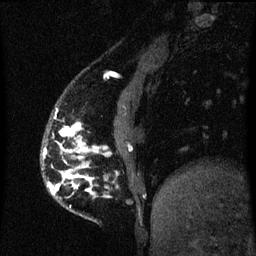
Breast MRI (dynamic contrast-enhanced), one sagittal slice; slice 13 of 60 in the series (ordered by position); dynamic contrast-enhanced series, image 2 of 3 at this slice position (ordered by acquisition); 1.5 T; TE 4.2 ms, TR 8 ms; 256 × 256 image matrix, field of view 190 × 190 mm. Female patient, age 50 years.
Outlined on this slice (semi-automatic segmentation, software-assisted and operator-edited):
- analysis volume of interest (the breast-tissue region the enhancement analysis was run in; not a lesion): bounding box (x1, y1, x2, y2) in pixels: (44, 122, 97, 199)
- tumour enhancement mask (voxels above the 70 % enhancement threshold inside the analysis volume of interest): (48, 123, 97, 194)